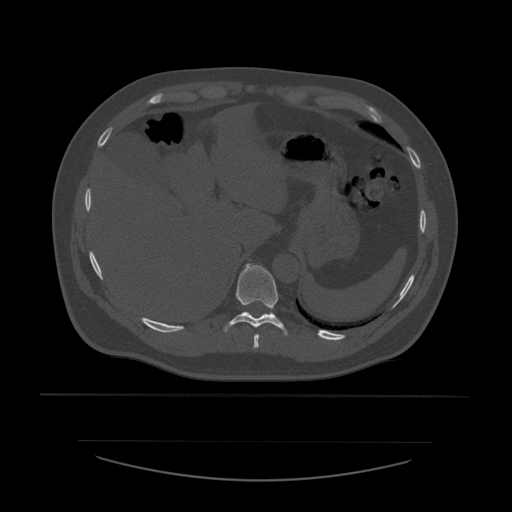
CT including the spine, one axial slice. Slice 297 of 532 in the series (ordered by position). Reconstruction kernel STANDARD. Bone window (W 1800 / L 400 HU). 512 × 512 image matrix, field of view 441 × 441 mm. Patient age 44 years. Case-level facts recorded for this patient, not image findings: primary cancer: soft tissue sarcoma.
Annotated regions visible in this slice (semi-automatic segmentation, software-assisted and operator-edited):
- T10 vertebra: bounding box (x1, y1, x2, y2) in pixels: (224, 264, 289, 336)
- T9 vertebra: (253, 334, 260, 350)